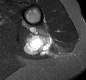
MRI of an extremity soft-tissue mass, one axial slice. Position 8 of 30 along the scan axis. STIR. MR volume resampled by the dataset authors to the PET/CT grid (not the native acquisition matrix). 3.27 mm slice thickness. 86 × 80 image matrix, field of view 84 × 78 mm. Female patient. From the clinical record (not read from this slice): histological type: malignant fibrous histiocytoma; grade: low; site of the primary tumour: left arm.
Outlined on this slice (expert contour drawn on MRI and transferred to this co-registered scan by the dataset authors):
- gross tumour volume (mass): bounding box (x1, y1, x2, y2) in pixels: (24, 26, 54, 55)